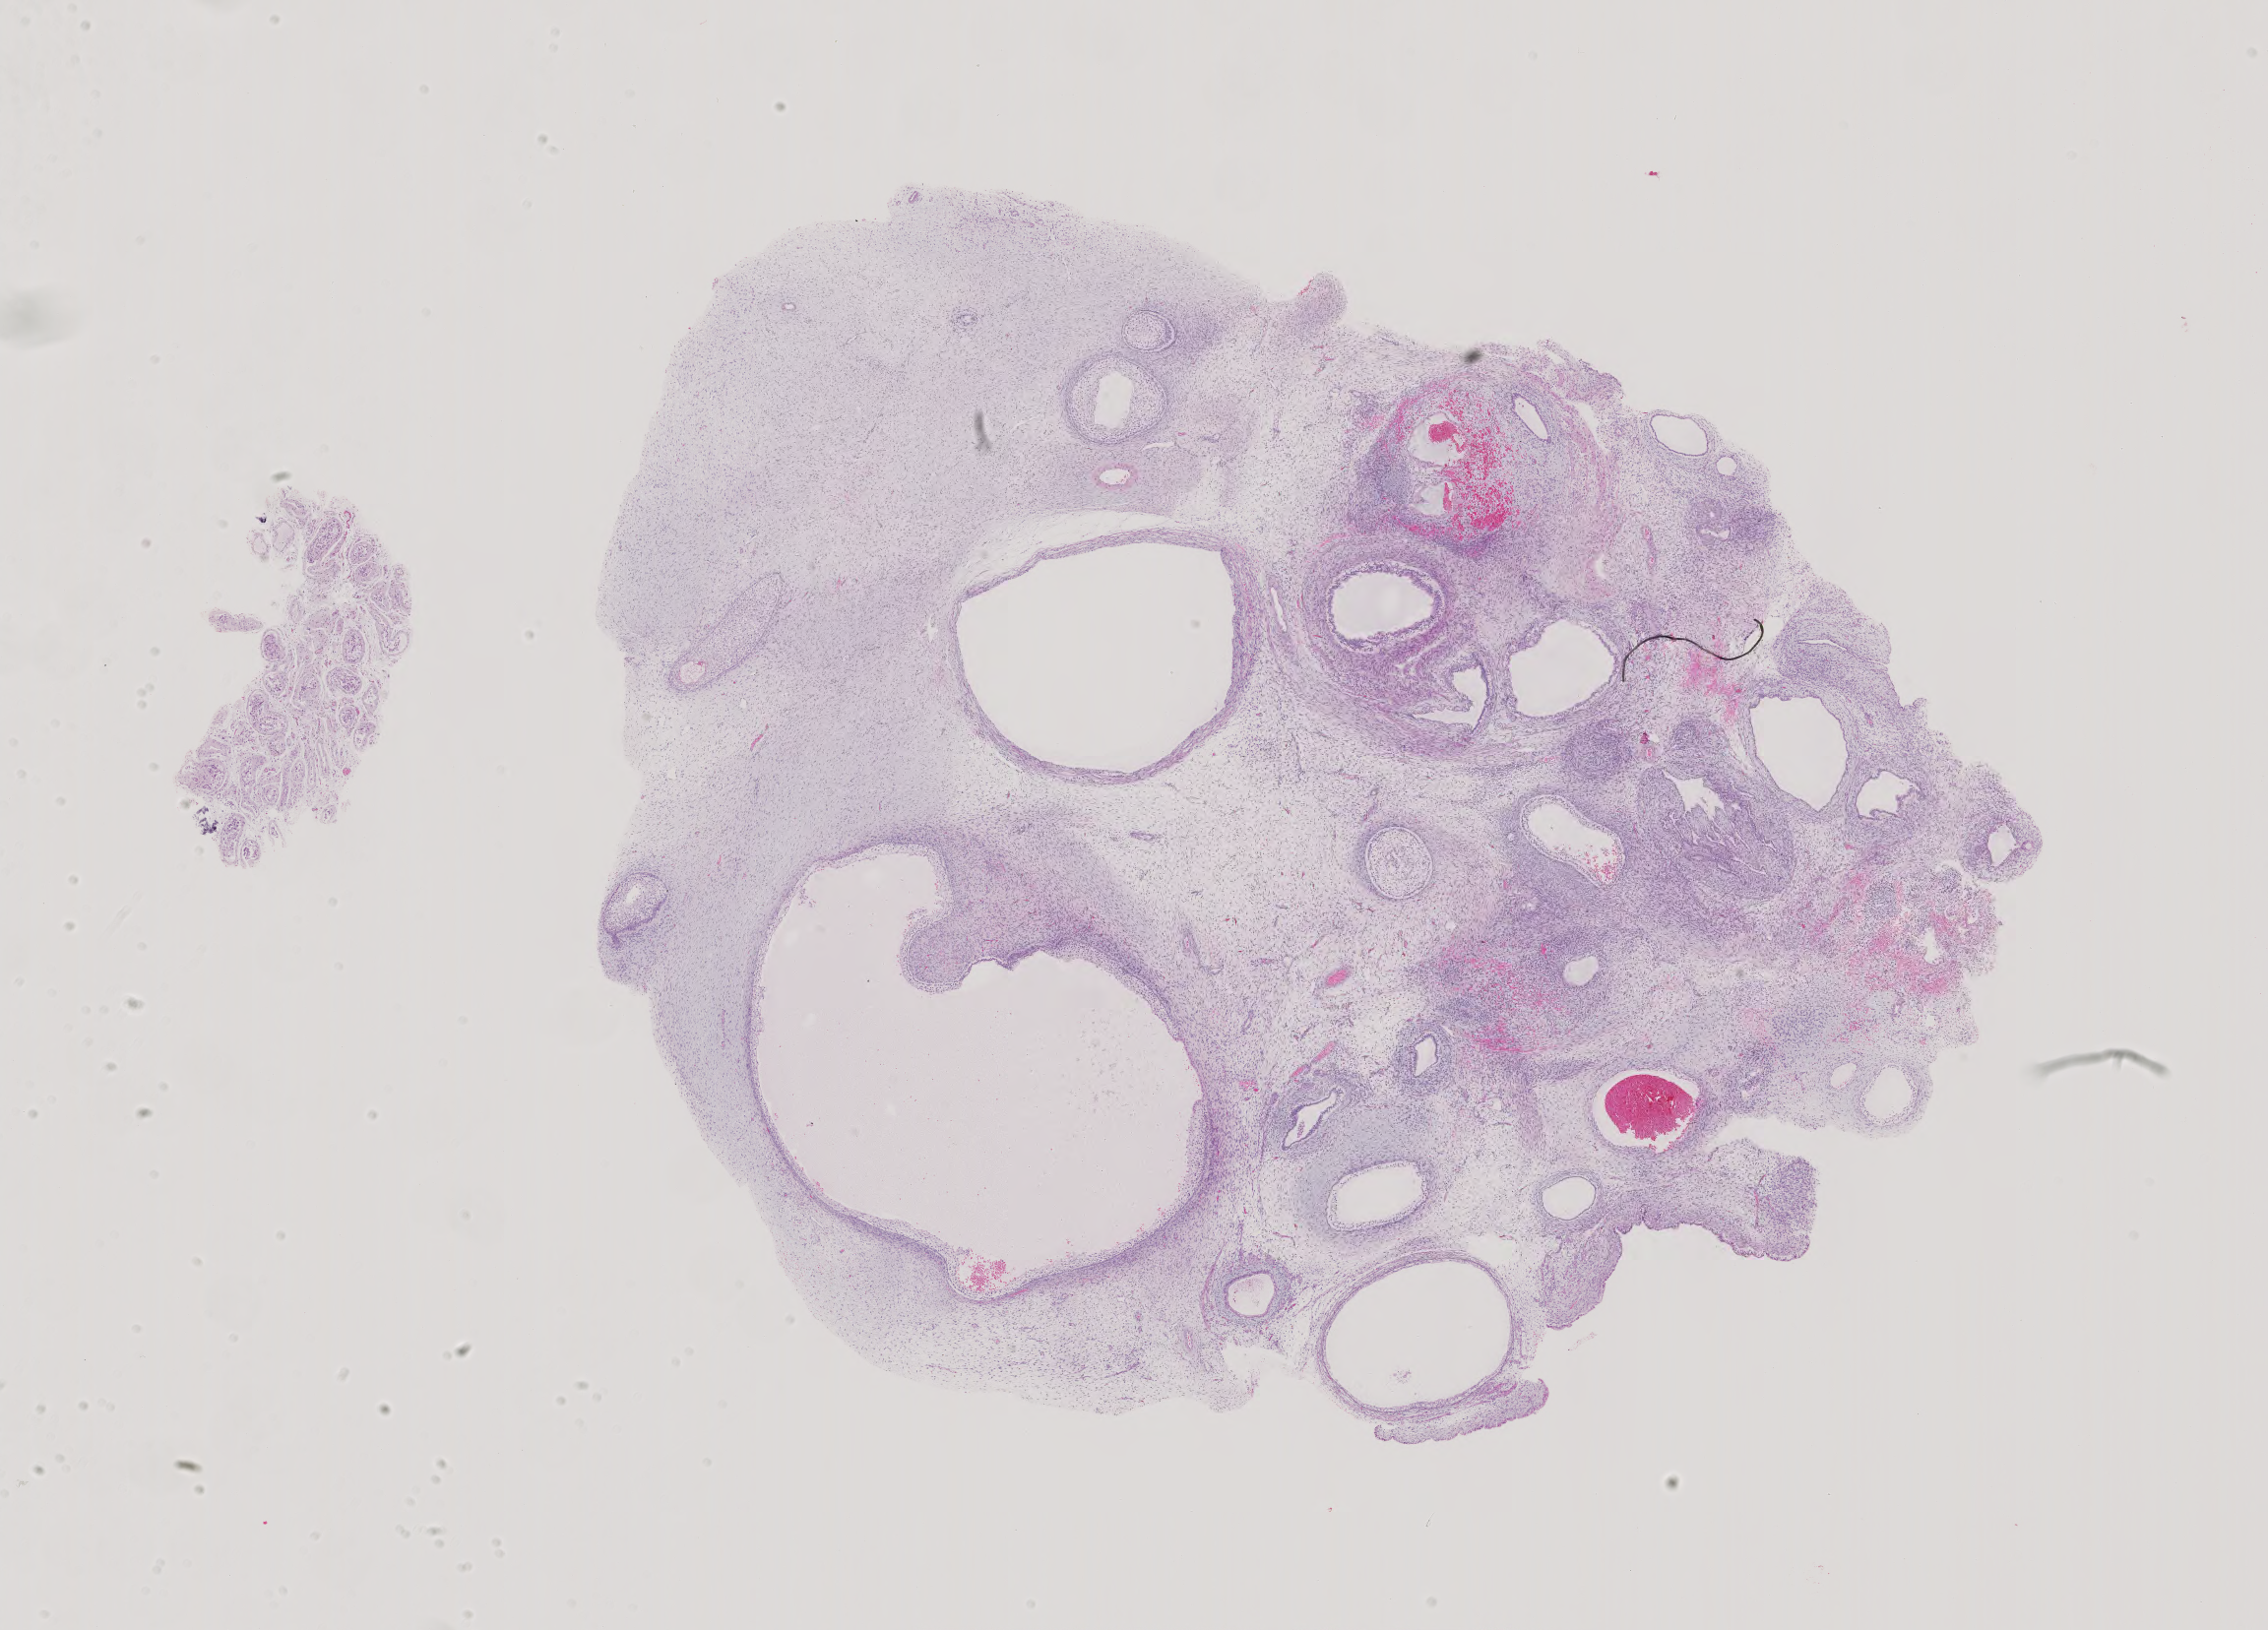
Digitized H&E tissue section (whole slide) — low-resolution overview of the scanned area, about 16.8 x 12.1 mm (from a 40x scan), formalin-fixed paraffin-embedded (FFPE) diagnostic section, testis, primary tumour sample. Male patient; age at initial diagnosis 22 years.
Histologic diagnosis: Teratoma, benign. AJCC pathologic stage: IA (5th edition). TNM: T1 N0 M0.